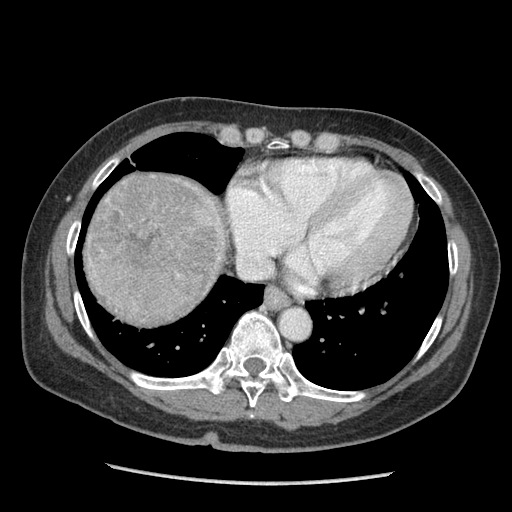
Contrast-enhanced abdominal CT (liver protocol), one axial slice; position 88 of 105 along the scan axis; reconstruction kernel STANDARD; soft-tissue window (W 400 / L 40 HU); 2.5 mm slice thickness; 512 × 512 image matrix, field of view 340 × 340 mm. From the clinical record (not read from this slice): diagnosis: hepatocellular carcinoma (patient treated with transarterial chemoembolisation; whether this scan precedes or follows treatment is not stated here); TNM stage (as recorded): Stage-I; Child-Pugh class: A; tumour differentiation: moderately differentiated; tumour nodularity: uninodular.
Structures marked on this image (semi-automatically segmented with operator editing):
- liver parenchyma outside the tumour (the mass and vessels are separate outlines, so this box may not span the whole liver): bounding box (x1, y1, x2, y2) in pixels: (84, 172, 223, 320)
- mass: (88, 176, 229, 324)